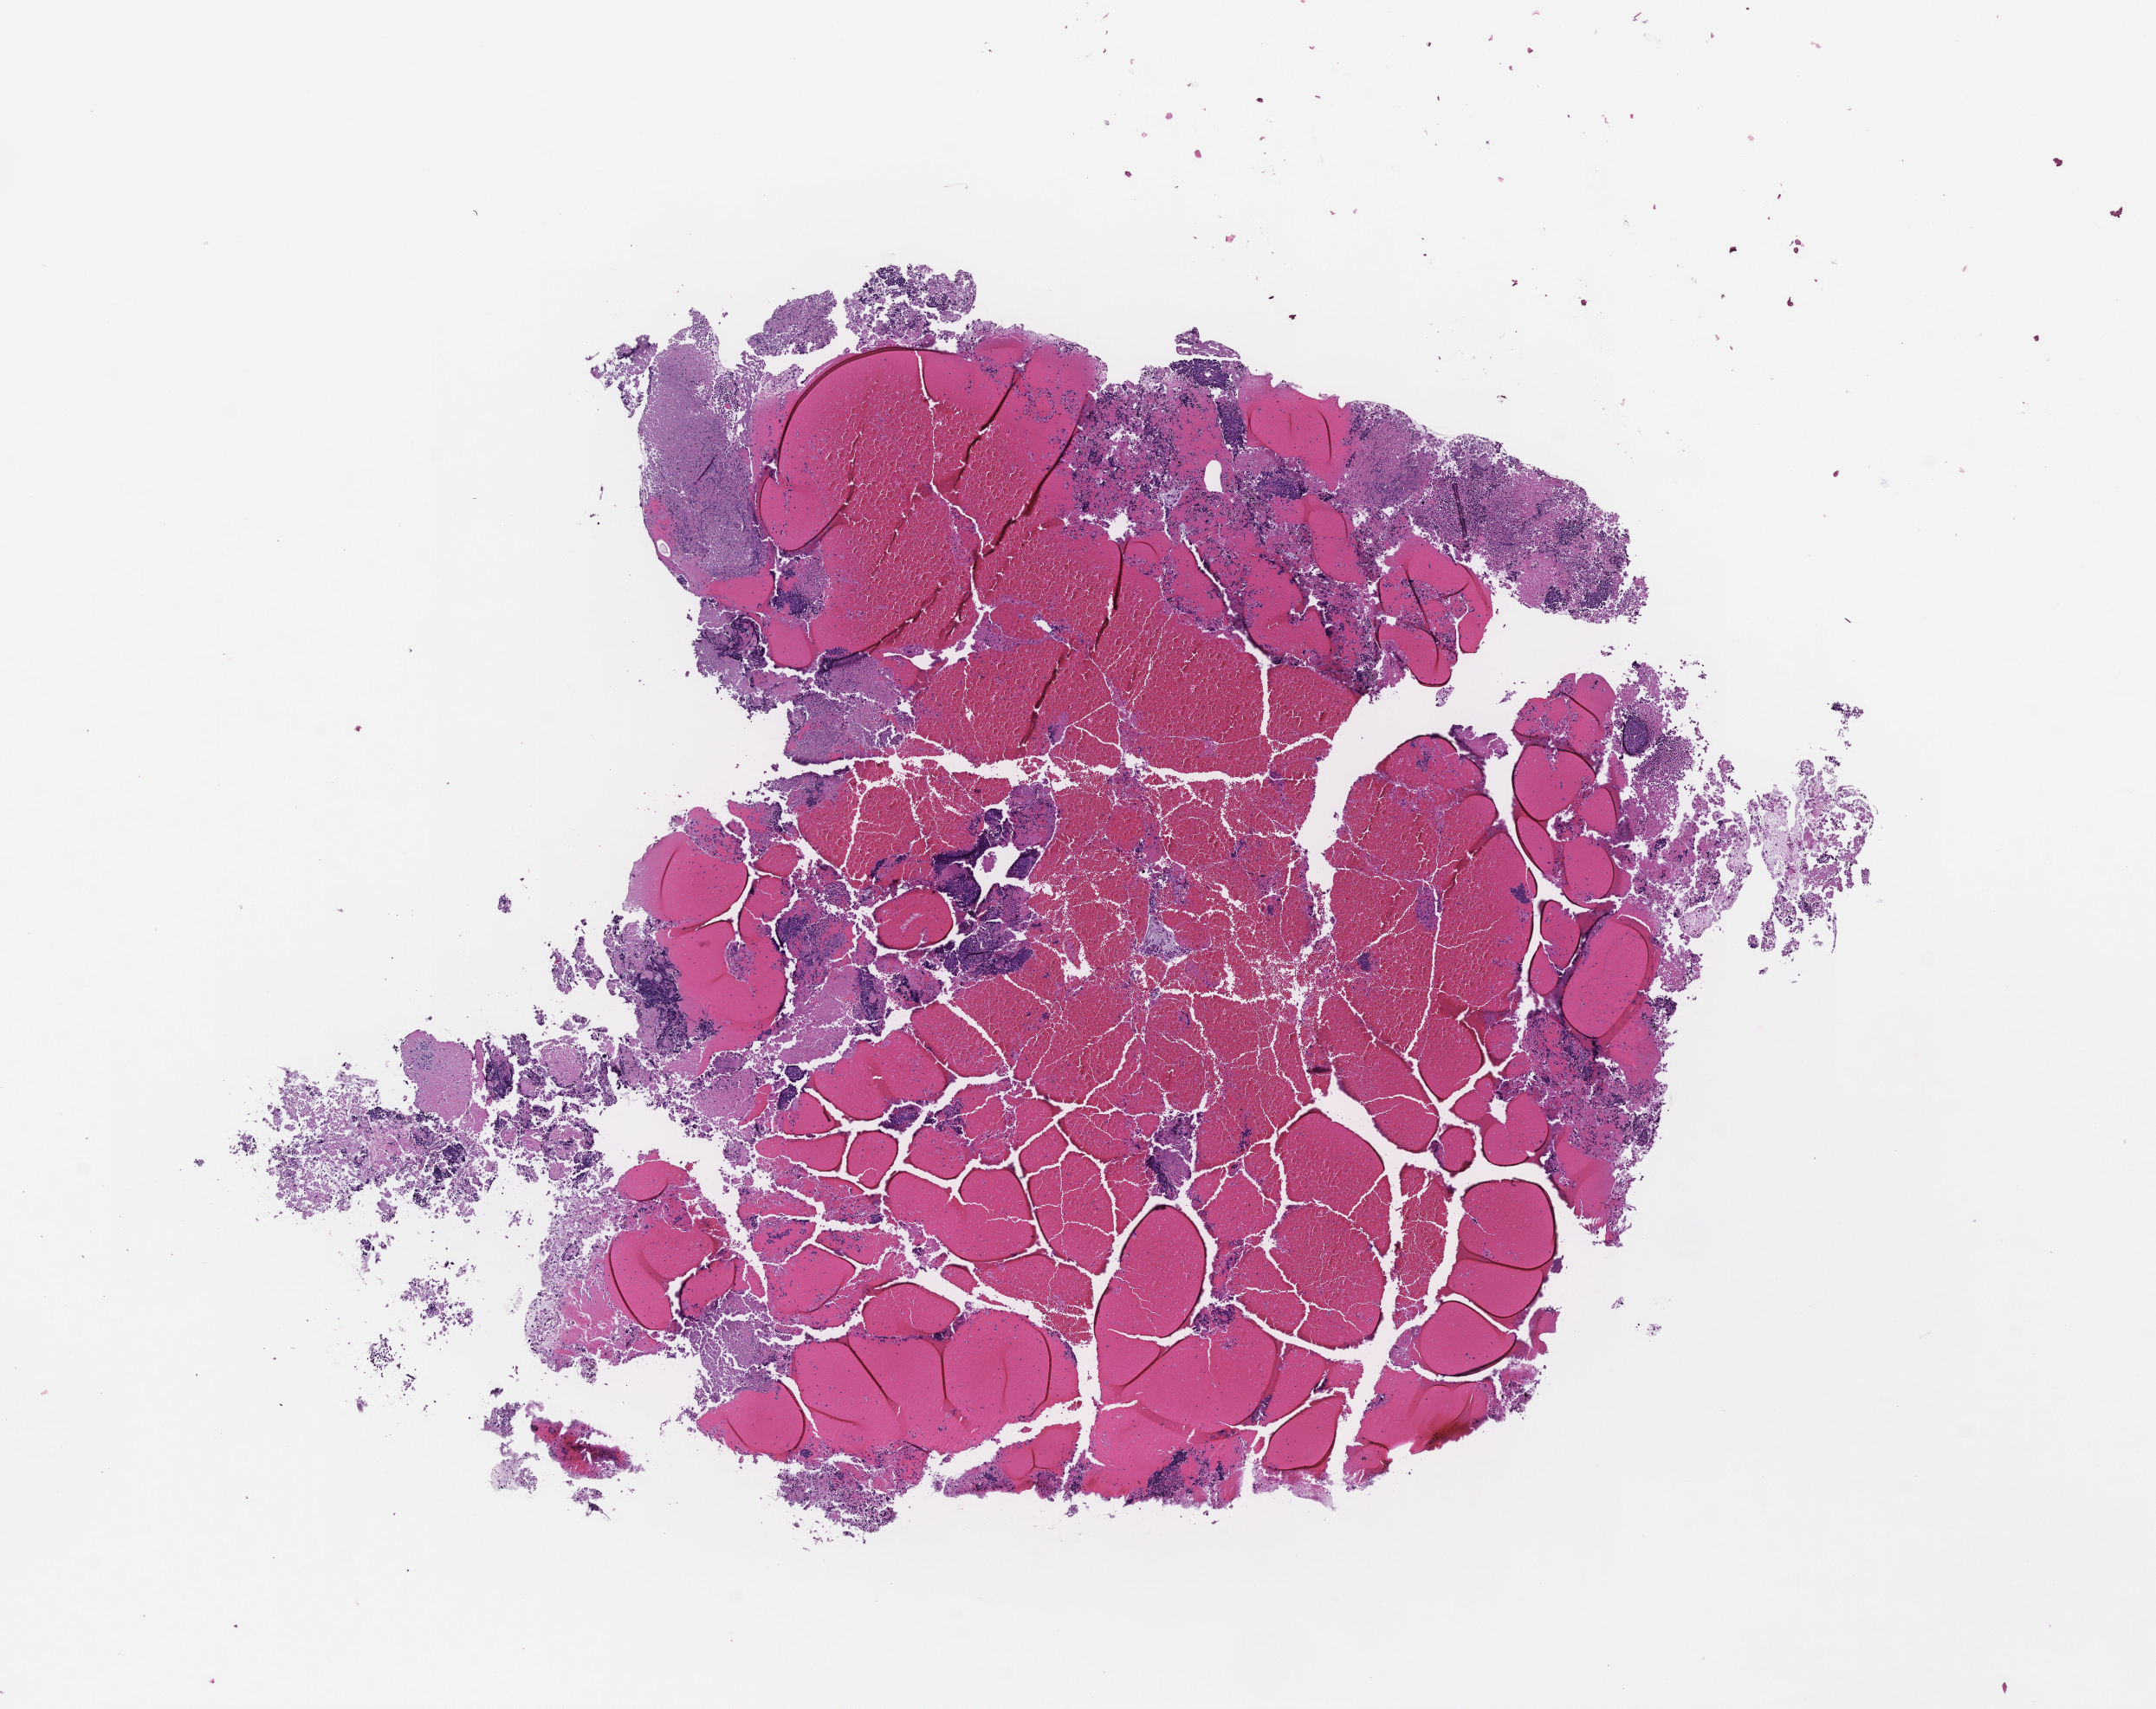
H&E whole-slide image, low-resolution overview of the scanned area, about 10.1 x 8.0 mm, FFPE section, tissue site: lung, specimen time point: archival tissue. Patient: female.
This section: primary tumour tissue. Diagnosis: Small Cell Lung Carcinoma.